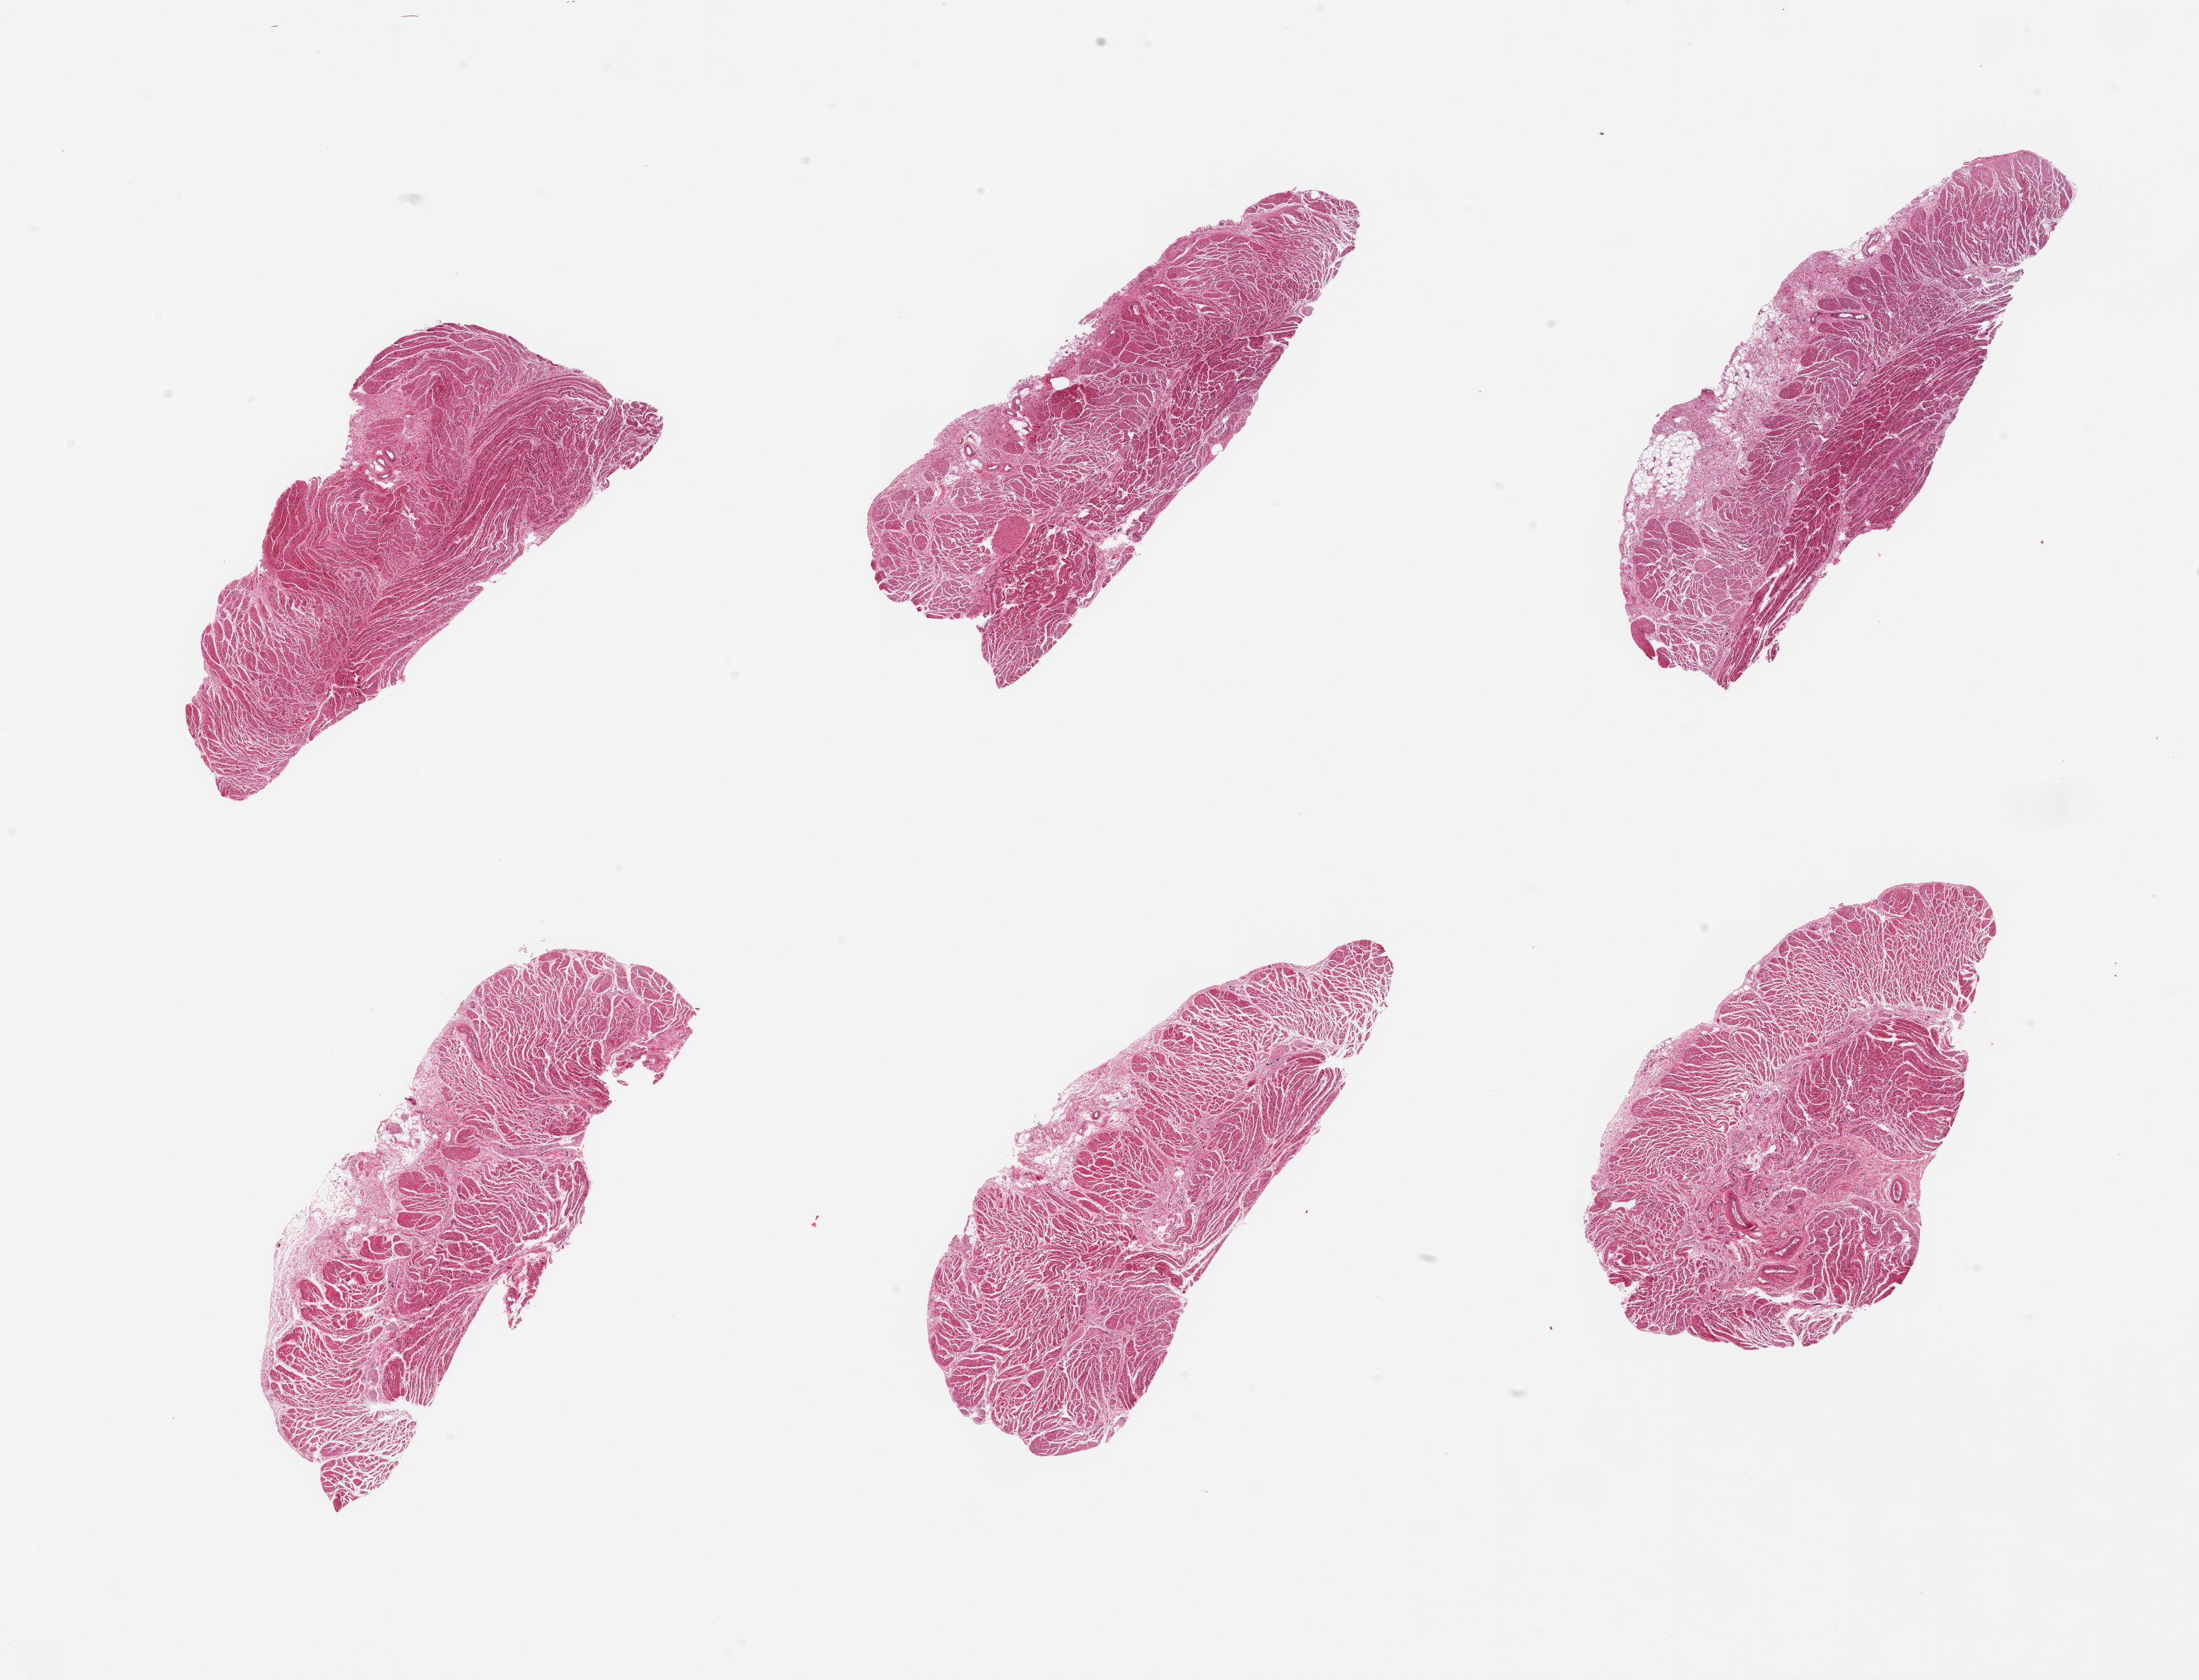
Whole-slide image, hematoxylin and eosin (H&E) stain, brightfield — a low-resolution overview of the entire scanned area, about 24.6 x 18.8 mm (from a 20x scan). PAXgene-fixed, paraffin-embedded tissue. Sampled site (target tissue): gastroesophageal junction. Tissue donor sample. Donor: female.
Reviewer comment on this tissue sample: 6 pieces; well trimmed muscularis.